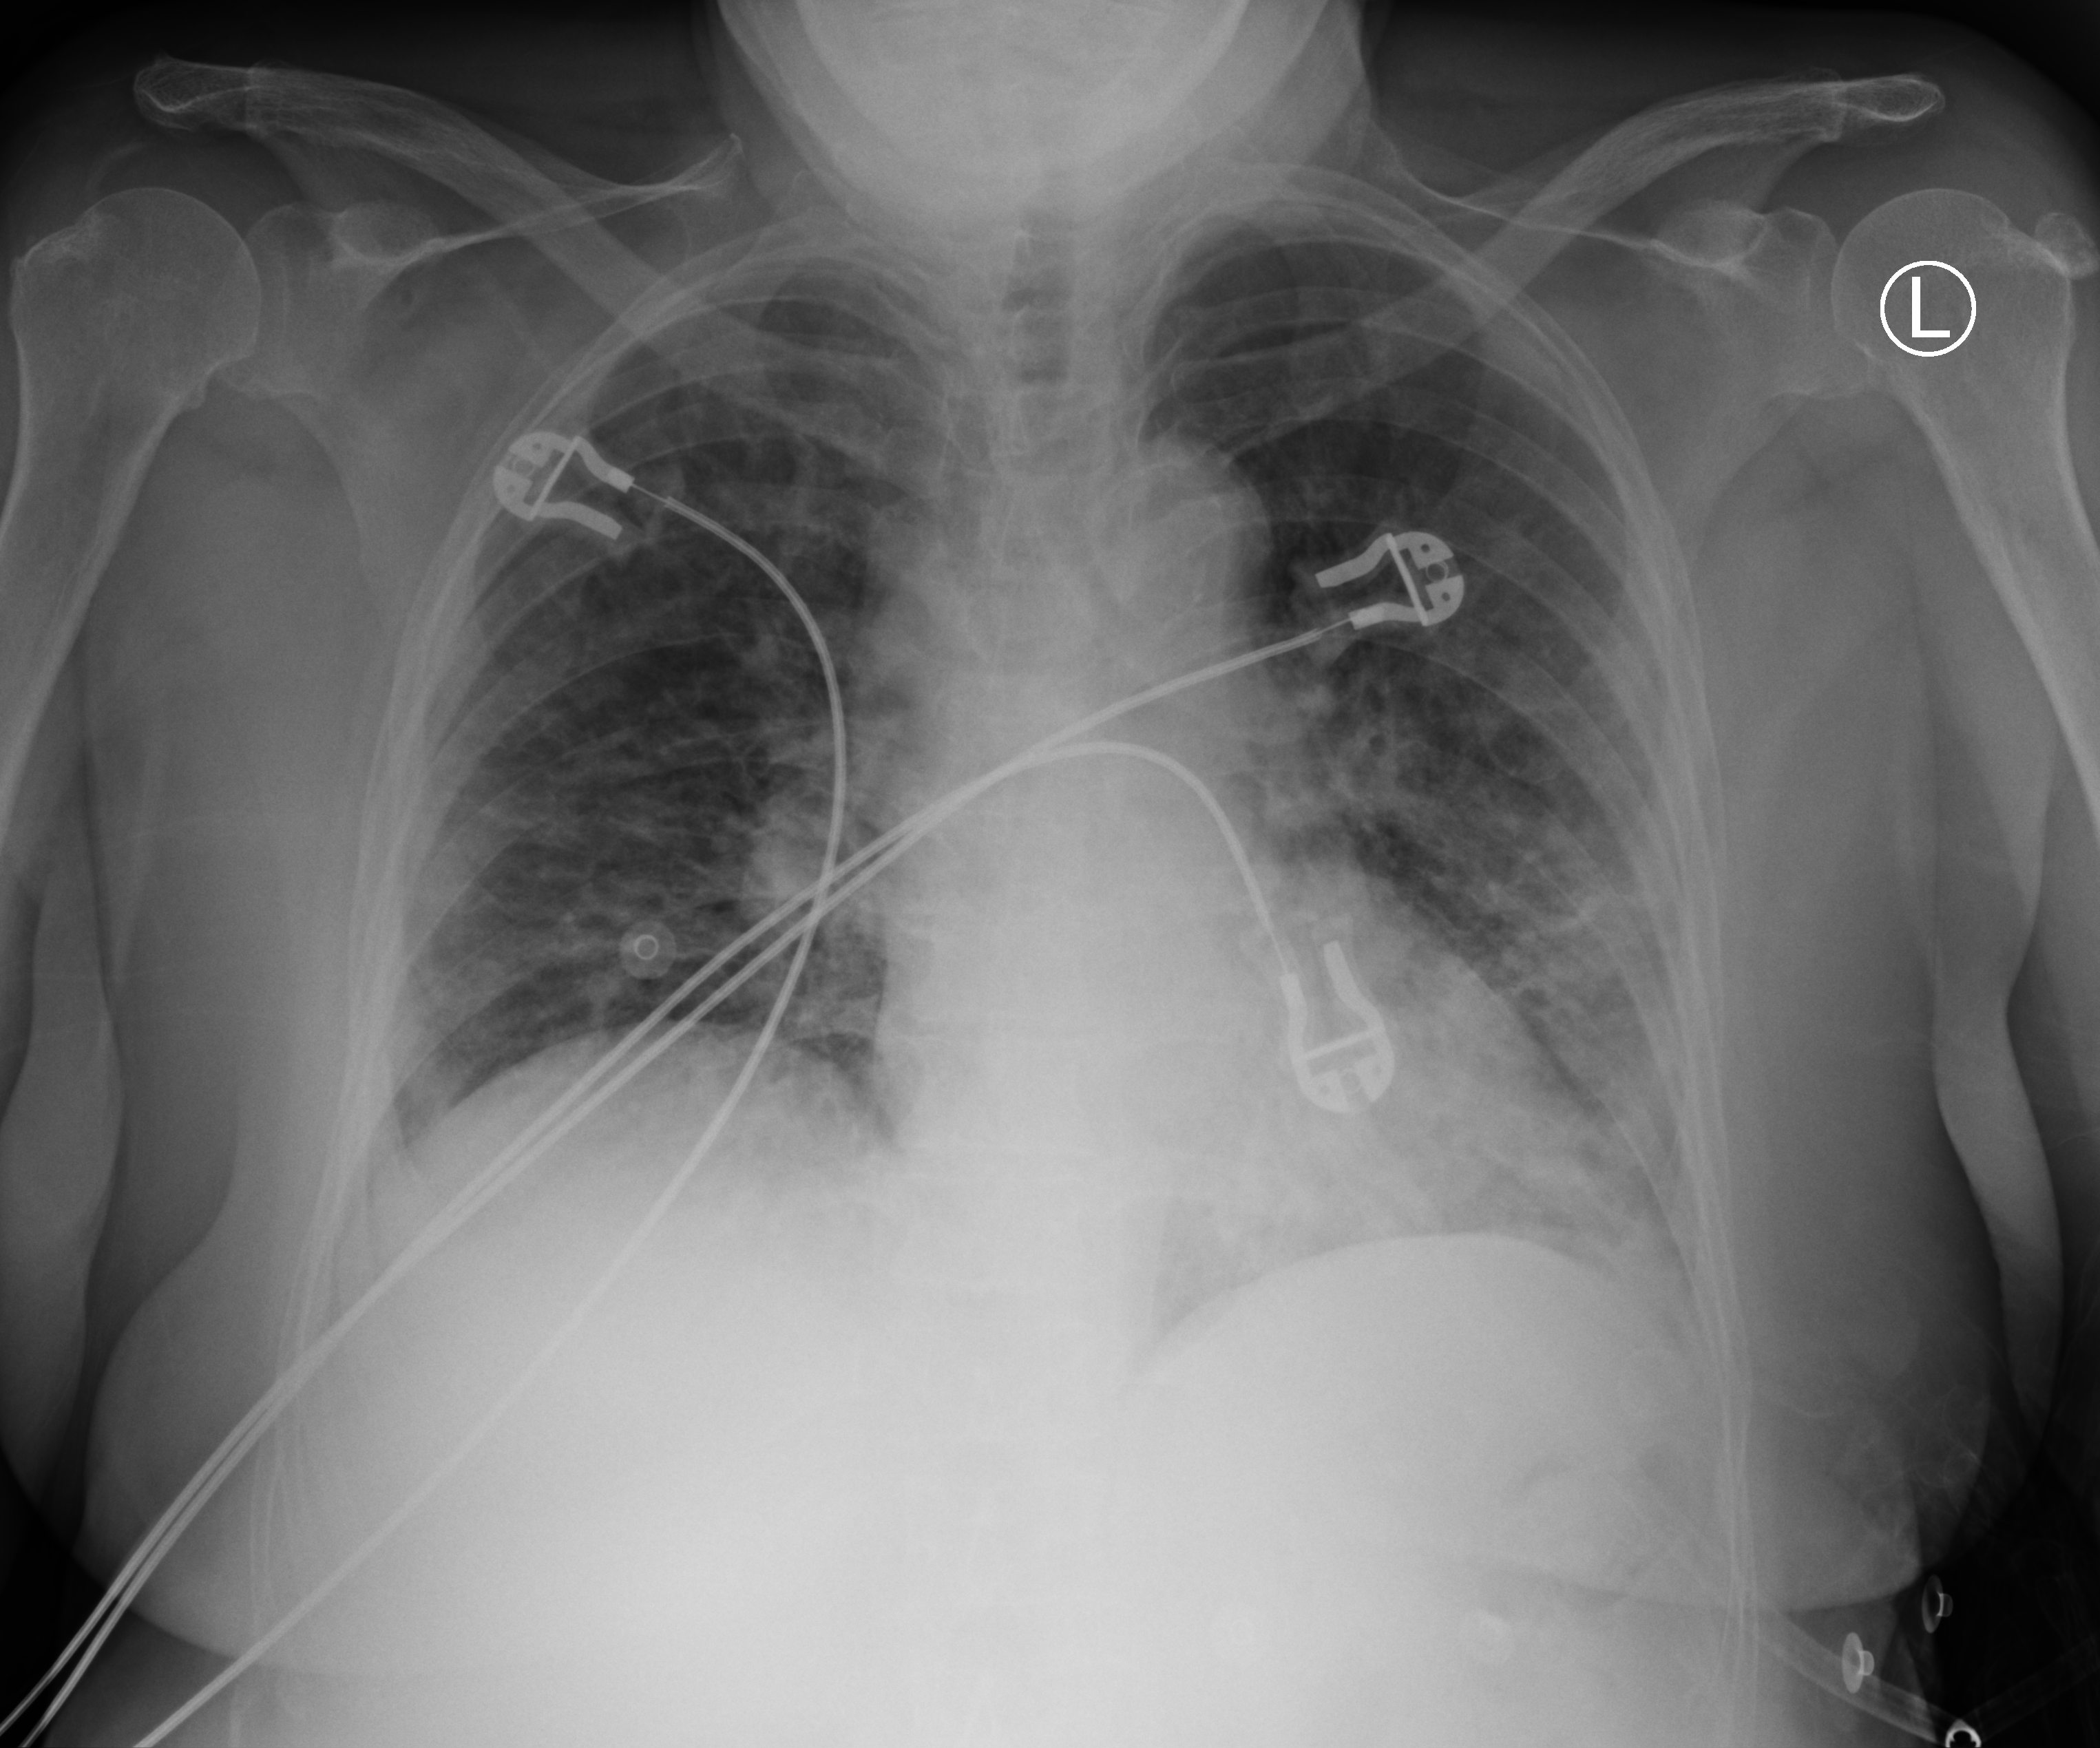
Chest X-ray (portable). Female patient hospitalised with COVID-19, age 75–90 years.
Hospital-stay facts (about this admission, not read from this image; timing relative to this image not recorded):
- diabetes (admission record): yes